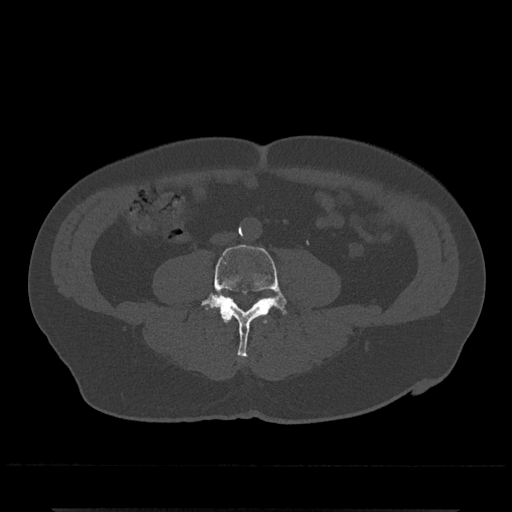
CT including the spine, one axial slice; slice 150 of 797 in the series (ordered by position); bone window (W 1800 / L 400 HU); 512 × 512 image matrix, field of view 393 × 393 mm. Patient: male, 67 years. From the clinical record (not read from this slice): primary cancer: prostate.
Outlined on this slice (semi-automatic segmentation, software-assisted and operator-edited):
- L3 vertebra: bounding box (x1, y1, x2, y2) in pixels: (223, 317, 267, 323)
- L4 vertebra: (201, 244, 287, 358)